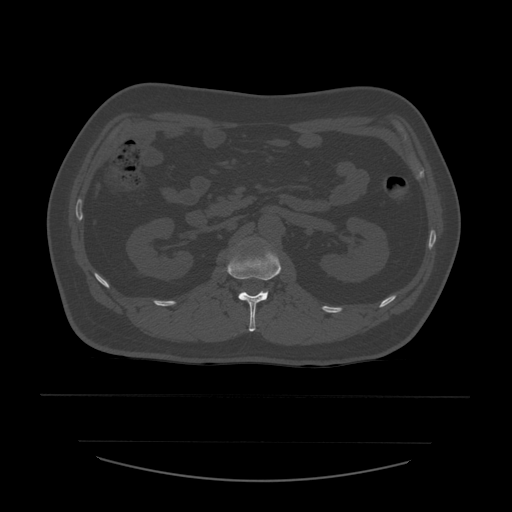
CT including the spine, one axial slice. Slice 220 of 532 in the series (ordered by position). 120 kVp. Bone window (W 1800 / L 400 HU). 1.25 mm slice thickness. 512 × 512 image matrix, field of view 441 × 441 mm. Patient age 44 years. From the clinical record (not read from this slice): primary cancer: soft tissue sarcoma.
Annotated regions visible in this slice (semi-automatic segmentation, software-assisted and operator-edited):
- L1 vertebra: bounding box <227,244,298,332> (left, top, right, bottom; pixels)